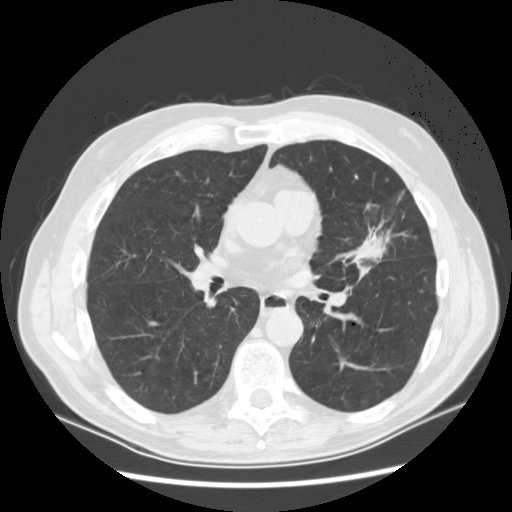
Axial slice from a low-dose chest CT screening exam; baseline annual screen; lung window (W 1500 / L -600 HU); slice 64 of 132 in the series. Male participant, aged 65 years at enrolment. Current smoker at enrolment.
Expert reader's lesion annotation, bounding box [x1, y1, x2, y2] px = [347, 201, 415, 271]. Reader record for this screening exam (exam-level; its link to the box is not recorded): non-calcified nodule or mass ≥4 mm, left upper lobe, 37 × 27 mm, spiculated (stellate) margins, soft tissue attenuation. Official screen result: positive, change unspecified: nodule(s) >= 4 mm or enlarging nodule(s), mass(es), or other non-specific abnormalities suspicious for lung cancer. Lung cancer was diagnosed 56 days after this screen: non-small cell carcinoma, poorly differentiated (G3), stage IA (AJCC 6th edition).